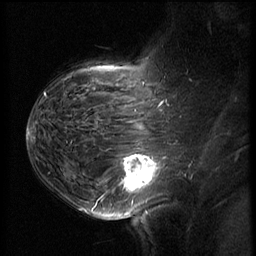
Breast MRI (dynamic contrast-enhanced), one sagittal slice; position 43 of 62 along the scan axis; 3 images stored at this slice position (order not interpretable as contrast timing); 1.5 T; TE 4.2 ms, TR 8.9 ms; 256 × 256 image matrix, field of view 200 × 200 mm. Patient: female, 37 years. Case-level facts recorded for this patient, not image findings: setting: breast cancer imaged before/during neoadjuvant chemotherapy; receptor status: triple-negative.
Outlined on this slice (semi-automatically segmented with operator editing):
- analysis volume of interest (the breast-tissue region the enhancement analysis was run in; not a lesion): bounding box [x1, y1, x2, y2] px = [116, 146, 168, 203]
- tumour enhancement mask (voxels above the 140 % enhancement threshold inside the analysis volume of interest): [122, 154, 160, 190]